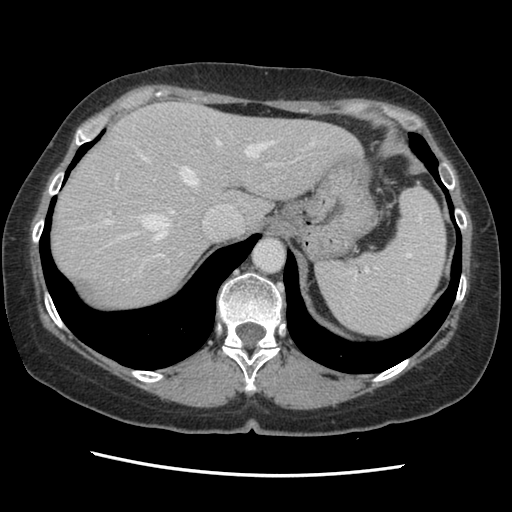
Contrast-enhanced abdominal CT, one axial slice. Slice 106 of 141 in the series (ordered by position). Soft-tissue window (W 400 / L 40 HU). 2.5 mm slice thickness. 512 × 512 image matrix, field of view 330 × 330 mm. Female patient, age 61 years. From the clinical record (not read from this slice): diagnosis: colorectal cancer liver metastases, imaged before liver resection; multiple liver metastases: no.
Annotated regions visible in this slice (expert manual segmentation):
- hepatic veins: bounding box <84,139,315,275> (left, top, right, bottom; pixels)
- liver: <52,102,359,312>
- planned liver remnant (the part of the liver to remain after resection): <52,103,359,312>
- portal vein (with intrahepatic branches): <107,163,279,270>